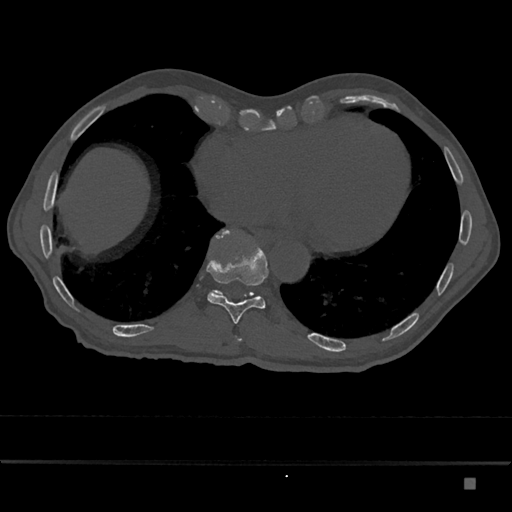
CT including the spine, one axial slice. Slice 733 of 797 in the series (ordered by position). Reconstruction kernel Br40s/3. Bone window (W 1800 / L 400 HU). 512 × 512 image matrix. Male patient, age 72 years. From the clinical record (not read from this slice): primary cancer: prostate.
Structures marked on this image (semi-automatically segmented with operator editing):
- T10 vertebra: bounding box (x1, y1, x2, y2) in pixels: (207, 235, 269, 324)
- T11 vertebra: (209, 229, 254, 297)
- T9 vertebra: (238, 338, 242, 341)